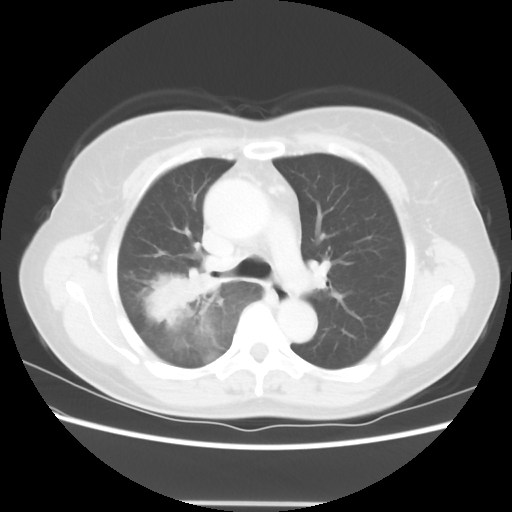
Chest CT, one axial slice; position 39 of 56 along the scan axis; reconstruction kernel STANDARD; 120 kVp; lung window (W 1500 / L -600 HU); 5 mm slice thickness; 512 × 512 image matrix, field of view 360 × 360 mm. Female patient, age 55 years. From the clinical record (not read from this slice): clinical TNM (as recorded): T2 N1 M0; histopathological grade: G2-3.
Outlined on this slice (rectangle marked by the reading radiologist):
- lung tumour (recorded histology: adenocarcinoma): box from (x=135, y=259) to (x=234, y=336) px